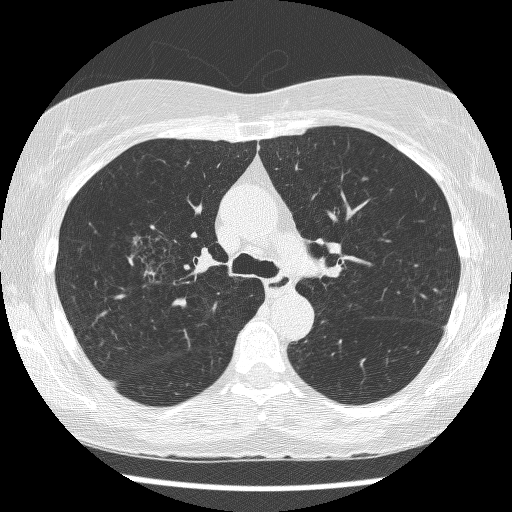
Low-dose screening chest CT, axial slice. Baseline screening round. Lung window (W 1500 / L -600 HU). Slice 184 of 271 in the series. 512 × 512 image matrix, field of view 316 × 316 mm. Female, age 64 years at enrolment.
Lesion marked by an expert reader, bounding box (x1, y1, x2, y2) in pixels: (126, 226, 208, 304). The screening reader recorded 3 non-calcified nodules or masses ≥4 mm on this exam; which of them this box marks is not recorded. Participant outcome: lung cancer diagnosed 735 days after this screen — adenocarcinoma, NOS, right upper lobe, right middle lobe, right hilum, stage IV (AJCC 6th edition), 85 mm at pathology.